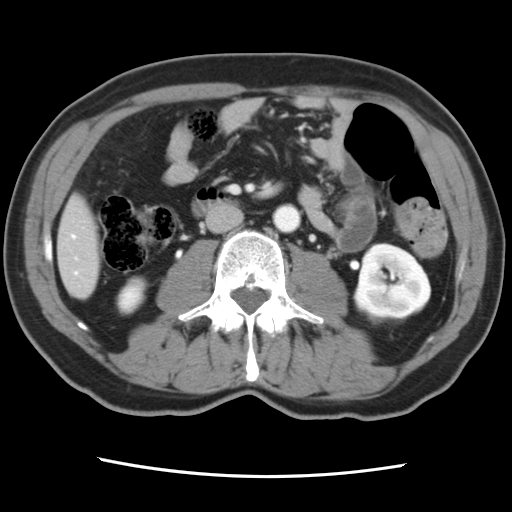
Contrast-enhanced abdominal CT, one axial slice. Position 19 of 83 along the scan axis. 120 kVp. Soft-tissue window (W 400 / L 40 HU). 512 × 512 image matrix, field of view 321 × 321 mm. Male patient, age 69 years. Case-level facts recorded for this patient, not image findings: diagnosis: colorectal cancer liver metastases, imaged before liver resection; multiple liver metastases: yes; largest metastasis: 3.5 cm; chemotherapy before resection: yes.
Structures marked on this image (manually delineated by an expert):
- hepatic veins: bounding box <72,235,77,275> (left, top, right, bottom; pixels)
- liver: <59,199,101,298>
- planned liver remnant (the part of the liver to remain after resection): <59,198,102,298>